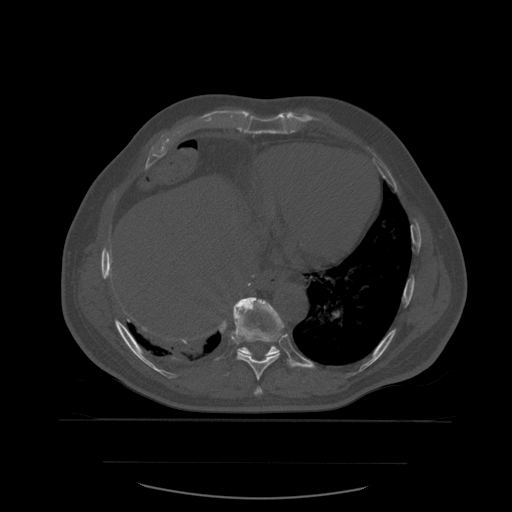
CT including the spine, one axial slice. Bone window (W 1800 / L 400 HU). 1.25 mm slice thickness. 512 × 512 image matrix. Patient age 71 years. Case-level facts recorded for this patient, not image findings: primary cancer: lung; vertebrae with lytic lesions (as recorded): T1, T2, L5, S1.
Structures marked on this image (semi-automatic segmentation, software-assisted and operator-edited):
- T10 vertebra: bounding box (x1, y1, x2, y2) in pixels: (233, 297, 285, 357)
- T8 vertebra: (255, 387, 263, 395)
- T9 vertebra: (227, 301, 282, 381)